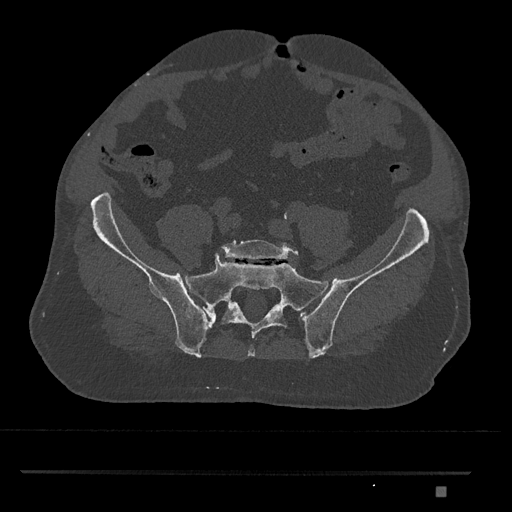
CT including the spine, one axial slice. Position 507 of 1134 along the scan axis. Reconstruction kernel Br40s/3. 120 kVp. Bone window (W 1800 / L 400 HU). 512 × 512 image matrix, field of view 429 × 429 mm. Male patient, age 65 years. From the clinical record (not read from this slice): primary cancer: prostate.
Annotated regions visible in this slice (semi-automatically segmented with operator editing):
- L5 vertebra: bounding box (x1, y1, x2, y2) in pixels: (219, 239, 299, 261)